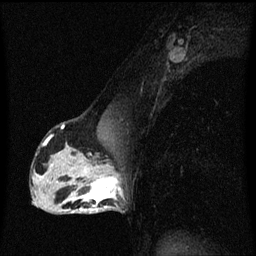
Breast MRI (dynamic contrast-enhanced), one sagittal slice; position 35 of 60 along the scan axis; dynamic contrast-enhanced series, image 2 of 3 at this slice position (ordered by acquisition); 1.5 T; TE 4.2 ms, TR 8.4 ms; 256 × 256 image matrix, field of view 200 × 200 mm. Female patient, age 40 years.
Structures marked on this image (semi-automatically segmented with operator editing):
- analysis volume of interest (the breast-tissue region the enhancement analysis was run in; not a lesion): bounding box [x1, y1, x2, y2] px = [76, 172, 123, 213]
- tumour enhancement mask (voxels above the 70 % enhancement threshold inside the analysis volume of interest): [76, 172, 123, 211]